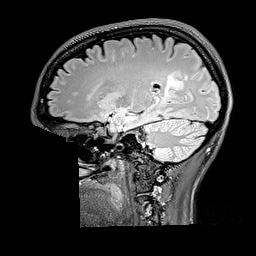
Brain MRI from a brain-tumour surgery series, one sagittal slice. Position 107 of 176 along the scan axis. T2 FLAIR. 1 mm slice thickness. 256 × 256 image matrix. Case-level facts recorded for this patient, not image findings: histopathology: Oligodendroglioma; WHO grade: 2; IDH mutation: yes.
Outlined on this slice (outlined manually by an expert reader):
- tumour: box from (x=161, y=73) to (x=185, y=103) px